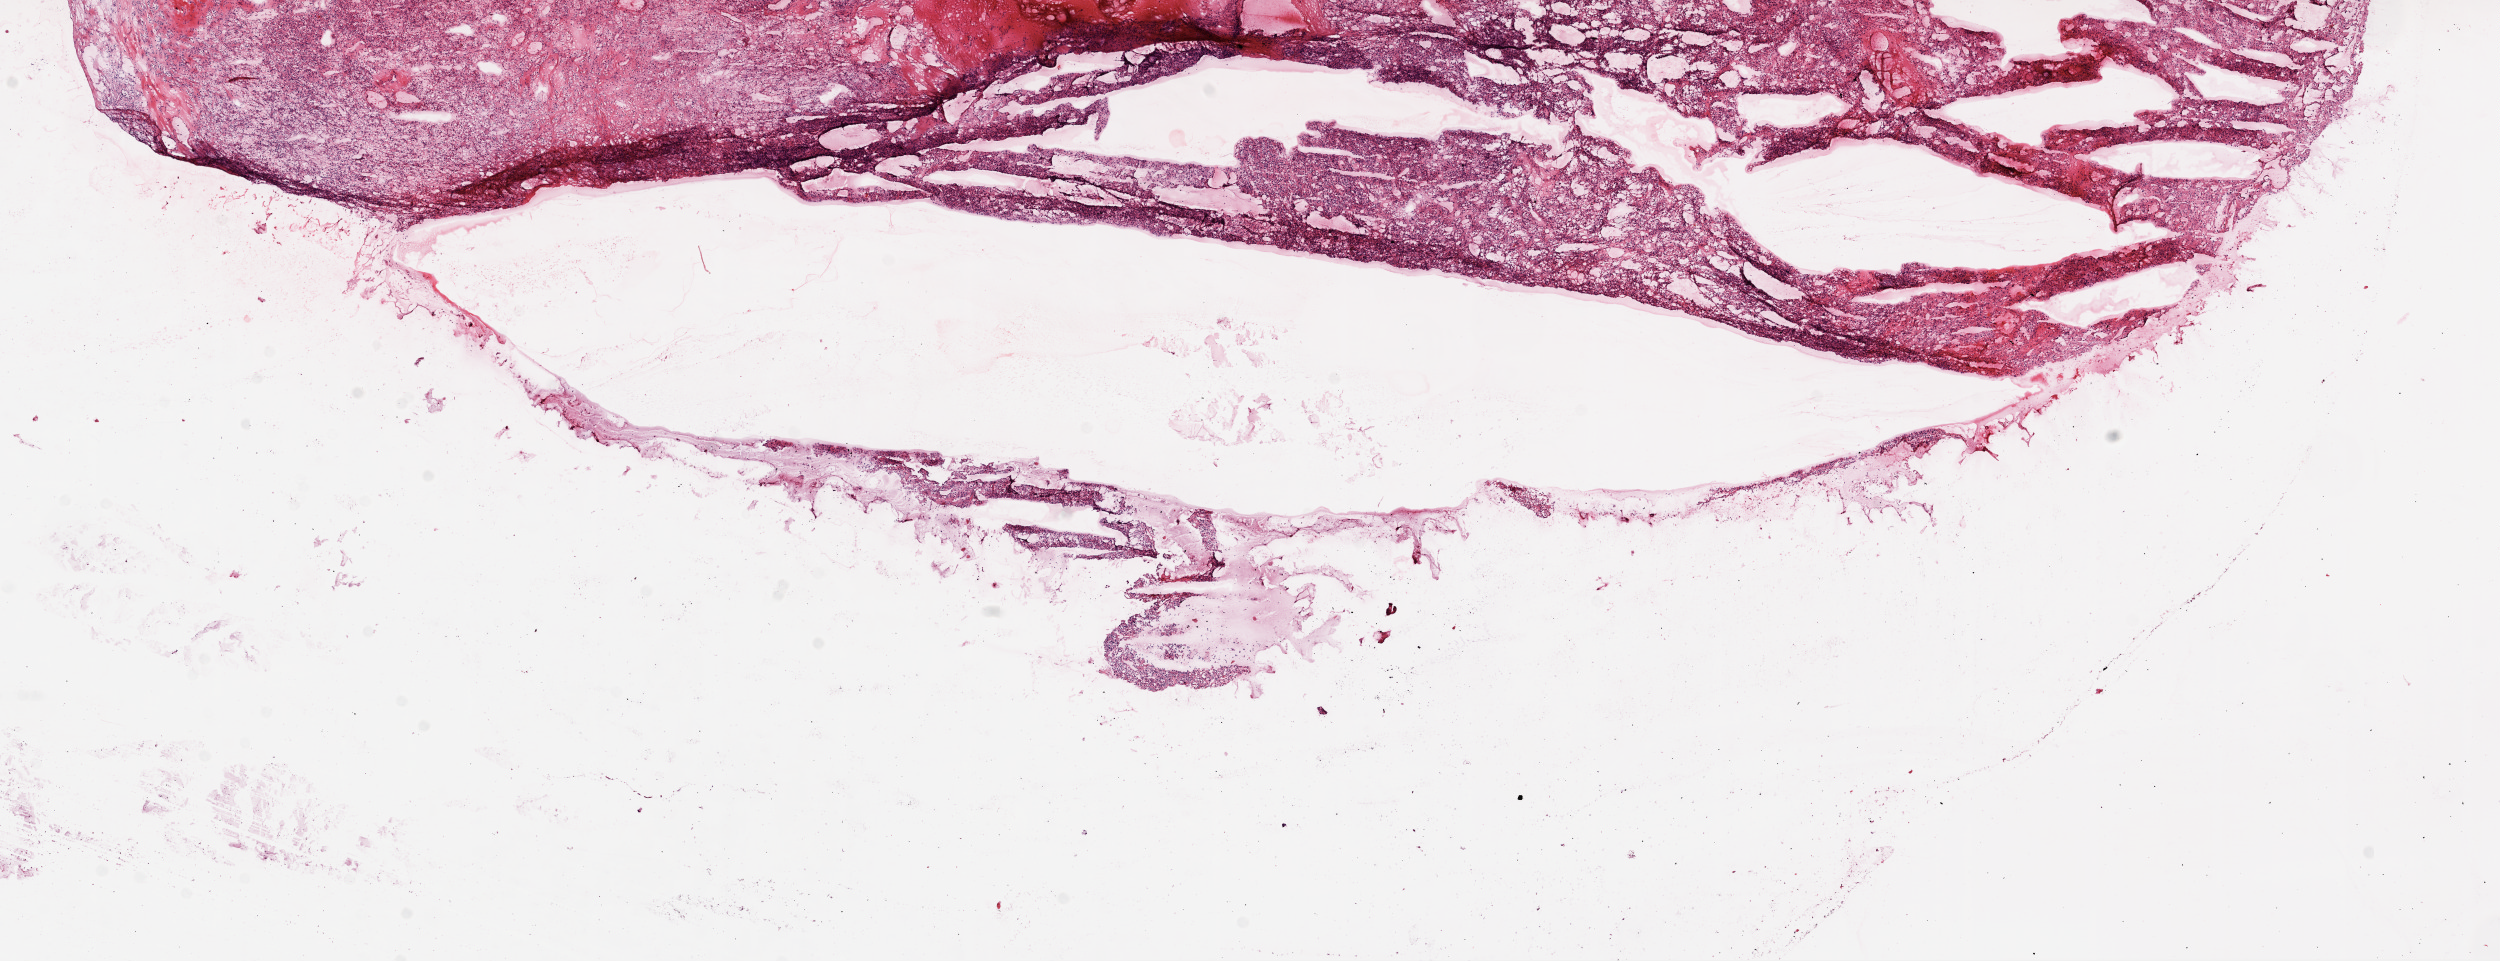
H&E whole-slide image, a low-resolution overview of the entire scanned area, about 20.1 x 7.7 mm (acquisition: 20x scan). Frozen section from the top of the tissue portion. Sample: primary tumour, kidney. Female patient; age at initial diagnosis 78 years. Histologic grade: G2 (moderately differentiated). Composition of this section per pathologist review: tumour cells 90%, tumour nuclei 85%, normal cells 0%, stromal cells 10%, necrosis 0%.
• AJCC pathologic stage: II
• diagnosis: Clear cell adenocarcinoma, NOS